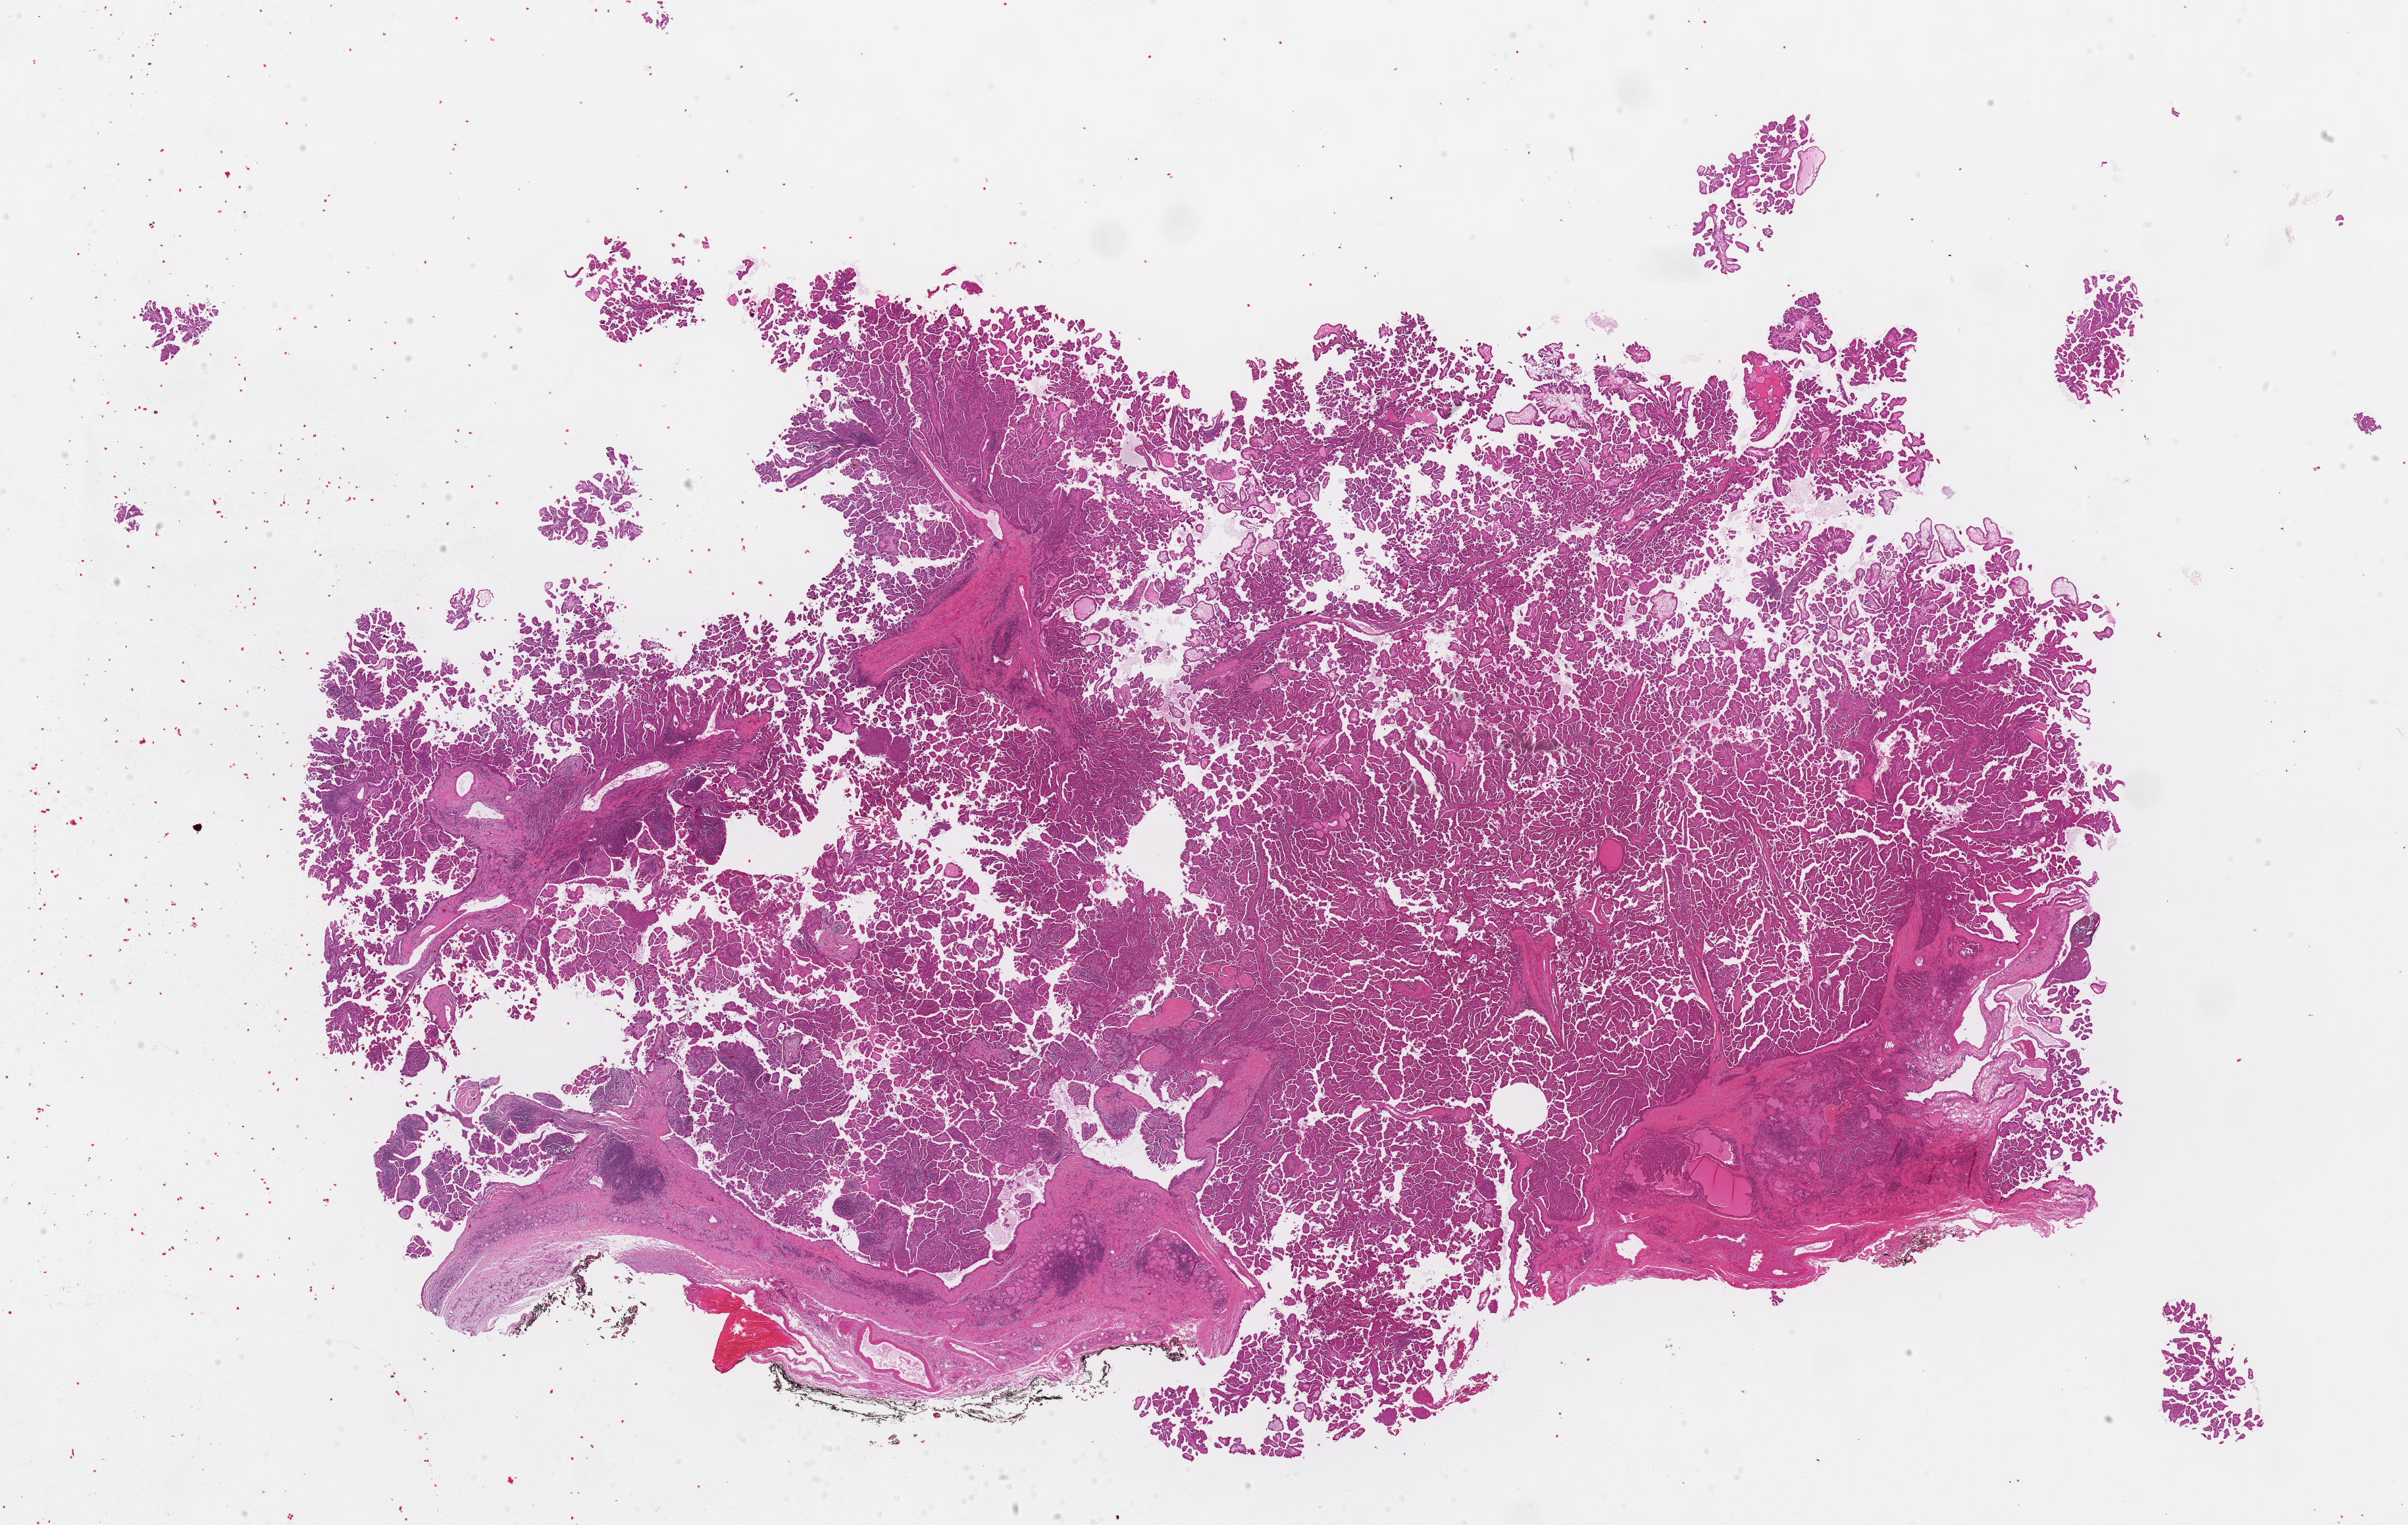
Hematoxylin and eosin (H&E) stained whole-slide image, shown as a low-resolution overview of the whole scanned area (about 28.9 x 18.3 mm, slide scanned at 40x), FFPE section, primary tumour sample from the thyroid. Patient: female, age at initial diagnosis 33 years.
Lymph nodes positive (case pathology): 12 of 19 examined. AJCC pathologic stage: I (7th edition). Laterality: left. Histologic diagnosis: Papillary adenocarcinoma, NOS (thyroid gland).